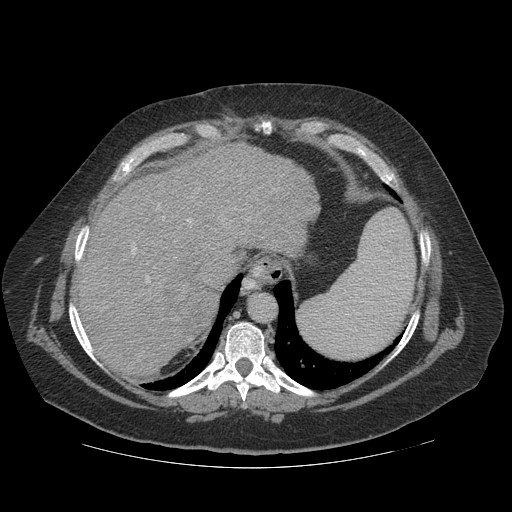
Contrast-enhanced abdominal CT (liver protocol), one axial slice. Slice 93 of 121 in the series (ordered by position). Reconstruction kernel STANDARD. 140 kVp. Soft-tissue window (W 400 / L 40 HU). 512 × 512 image matrix. From the clinical record (not read from this slice): diagnosis: hepatocellular carcinoma (patient treated with transarterial chemoembolisation; whether this scan precedes or follows treatment is not stated here); TNM stage (as recorded): Stage-IIIA; Child-Pugh class: A; tumour differentiation: well differentiated; tumour nodularity: multinodular.
Outlined on this slice (semi-automatic segmentation, software-assisted and operator-edited):
- abdominal aorta: box from (x=250, y=294) to (x=276, y=323) px
- liver parenchyma outside the tumour (the mass and vessels are separate outlines, so this box may not span the whole liver): (x=72, y=142)–(x=320, y=376)
- mass: (x=163, y=272)–(x=217, y=342)
- liver vessels: (x=131, y=202)–(x=242, y=283)